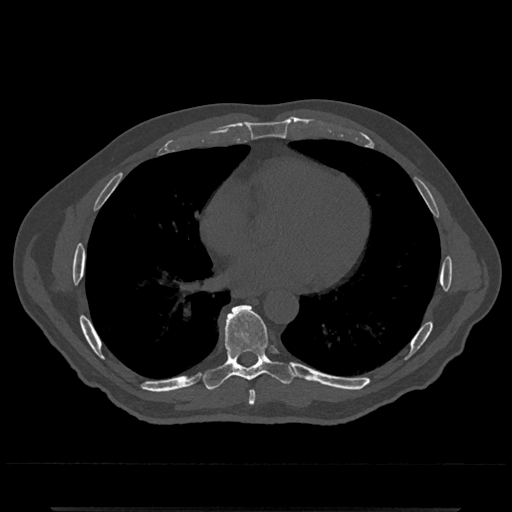
CT including the spine, one axial slice; slice 674 of 797 in the series (ordered by position); reconstruction kernel Br40s/3; bone window (W 1800 / L 400 HU); 0.5 mm slice thickness; 512 × 512 image matrix, field of view 393 × 393 mm. Male patient, age 67 years. From the clinical record (not read from this slice): primary cancer: prostate.
Structures marked on this image (semi-automatically segmented with operator editing):
- T7 vertebra: box from (x=248, y=390) to (x=256, y=406) px
- T8 vertebra: (x=203, y=305)–(x=295, y=390)